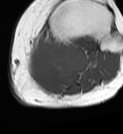
MRI of an extremity soft-tissue mass, one axial slice; slice 43 of 68 in the series (ordered by position); MR volume resampled by the dataset authors to the PET/CT grid (not the native acquisition matrix); 3.27 mm slice thickness; 123 × 134 image matrix. Female patient. Case-level facts recorded for this patient, not image findings: histological type: extraskeletal high grade osteogenic sarcoma; grade: high; site of the primary tumour: left calf.
Outlined on this slice (expert contour drawn on MRI and transferred to this co-registered scan by the dataset authors):
- gross tumour volume (mass): bounding box (x1, y1, x2, y2) in pixels: (26, 39, 89, 88)